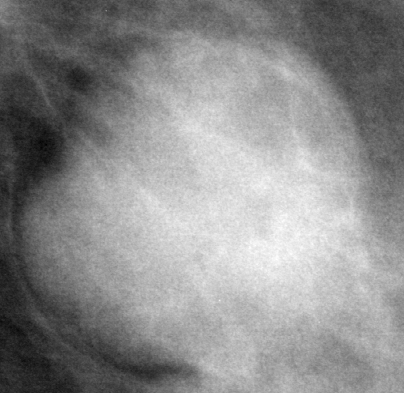
Region of interest cut from a scanned film mammogram (one marked finding), left breast, MLO view.
Finding: mass, shape round, margins circumscribed; BI-RADS assessment category 4; subtlety rating 5 on a 1 (subtle) to 5 (obvious) scale; pathology (as recorded): malignant.